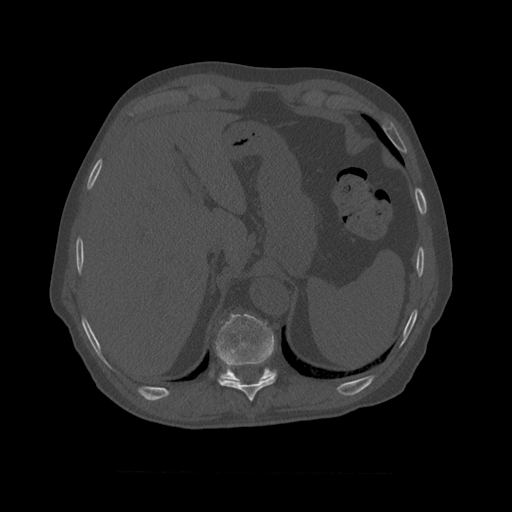
CT including the spine, one axial slice; position 415 of 450 along the scan axis; 120 kVp; bone window (W 1800 / L 400 HU); 1.25 mm slice thickness; 512 × 512 image matrix, field of view 405 × 405 mm. Patient age 75 years. From the clinical record (not read from this slice): primary cancer: prostate.
Annotated regions visible in this slice (semi-automatically segmented with operator editing):
- T10 vertebra: box from (x=216, y=314) to (x=277, y=382) px
- T9 vertebra: (x=217, y=362)–(x=278, y=402)